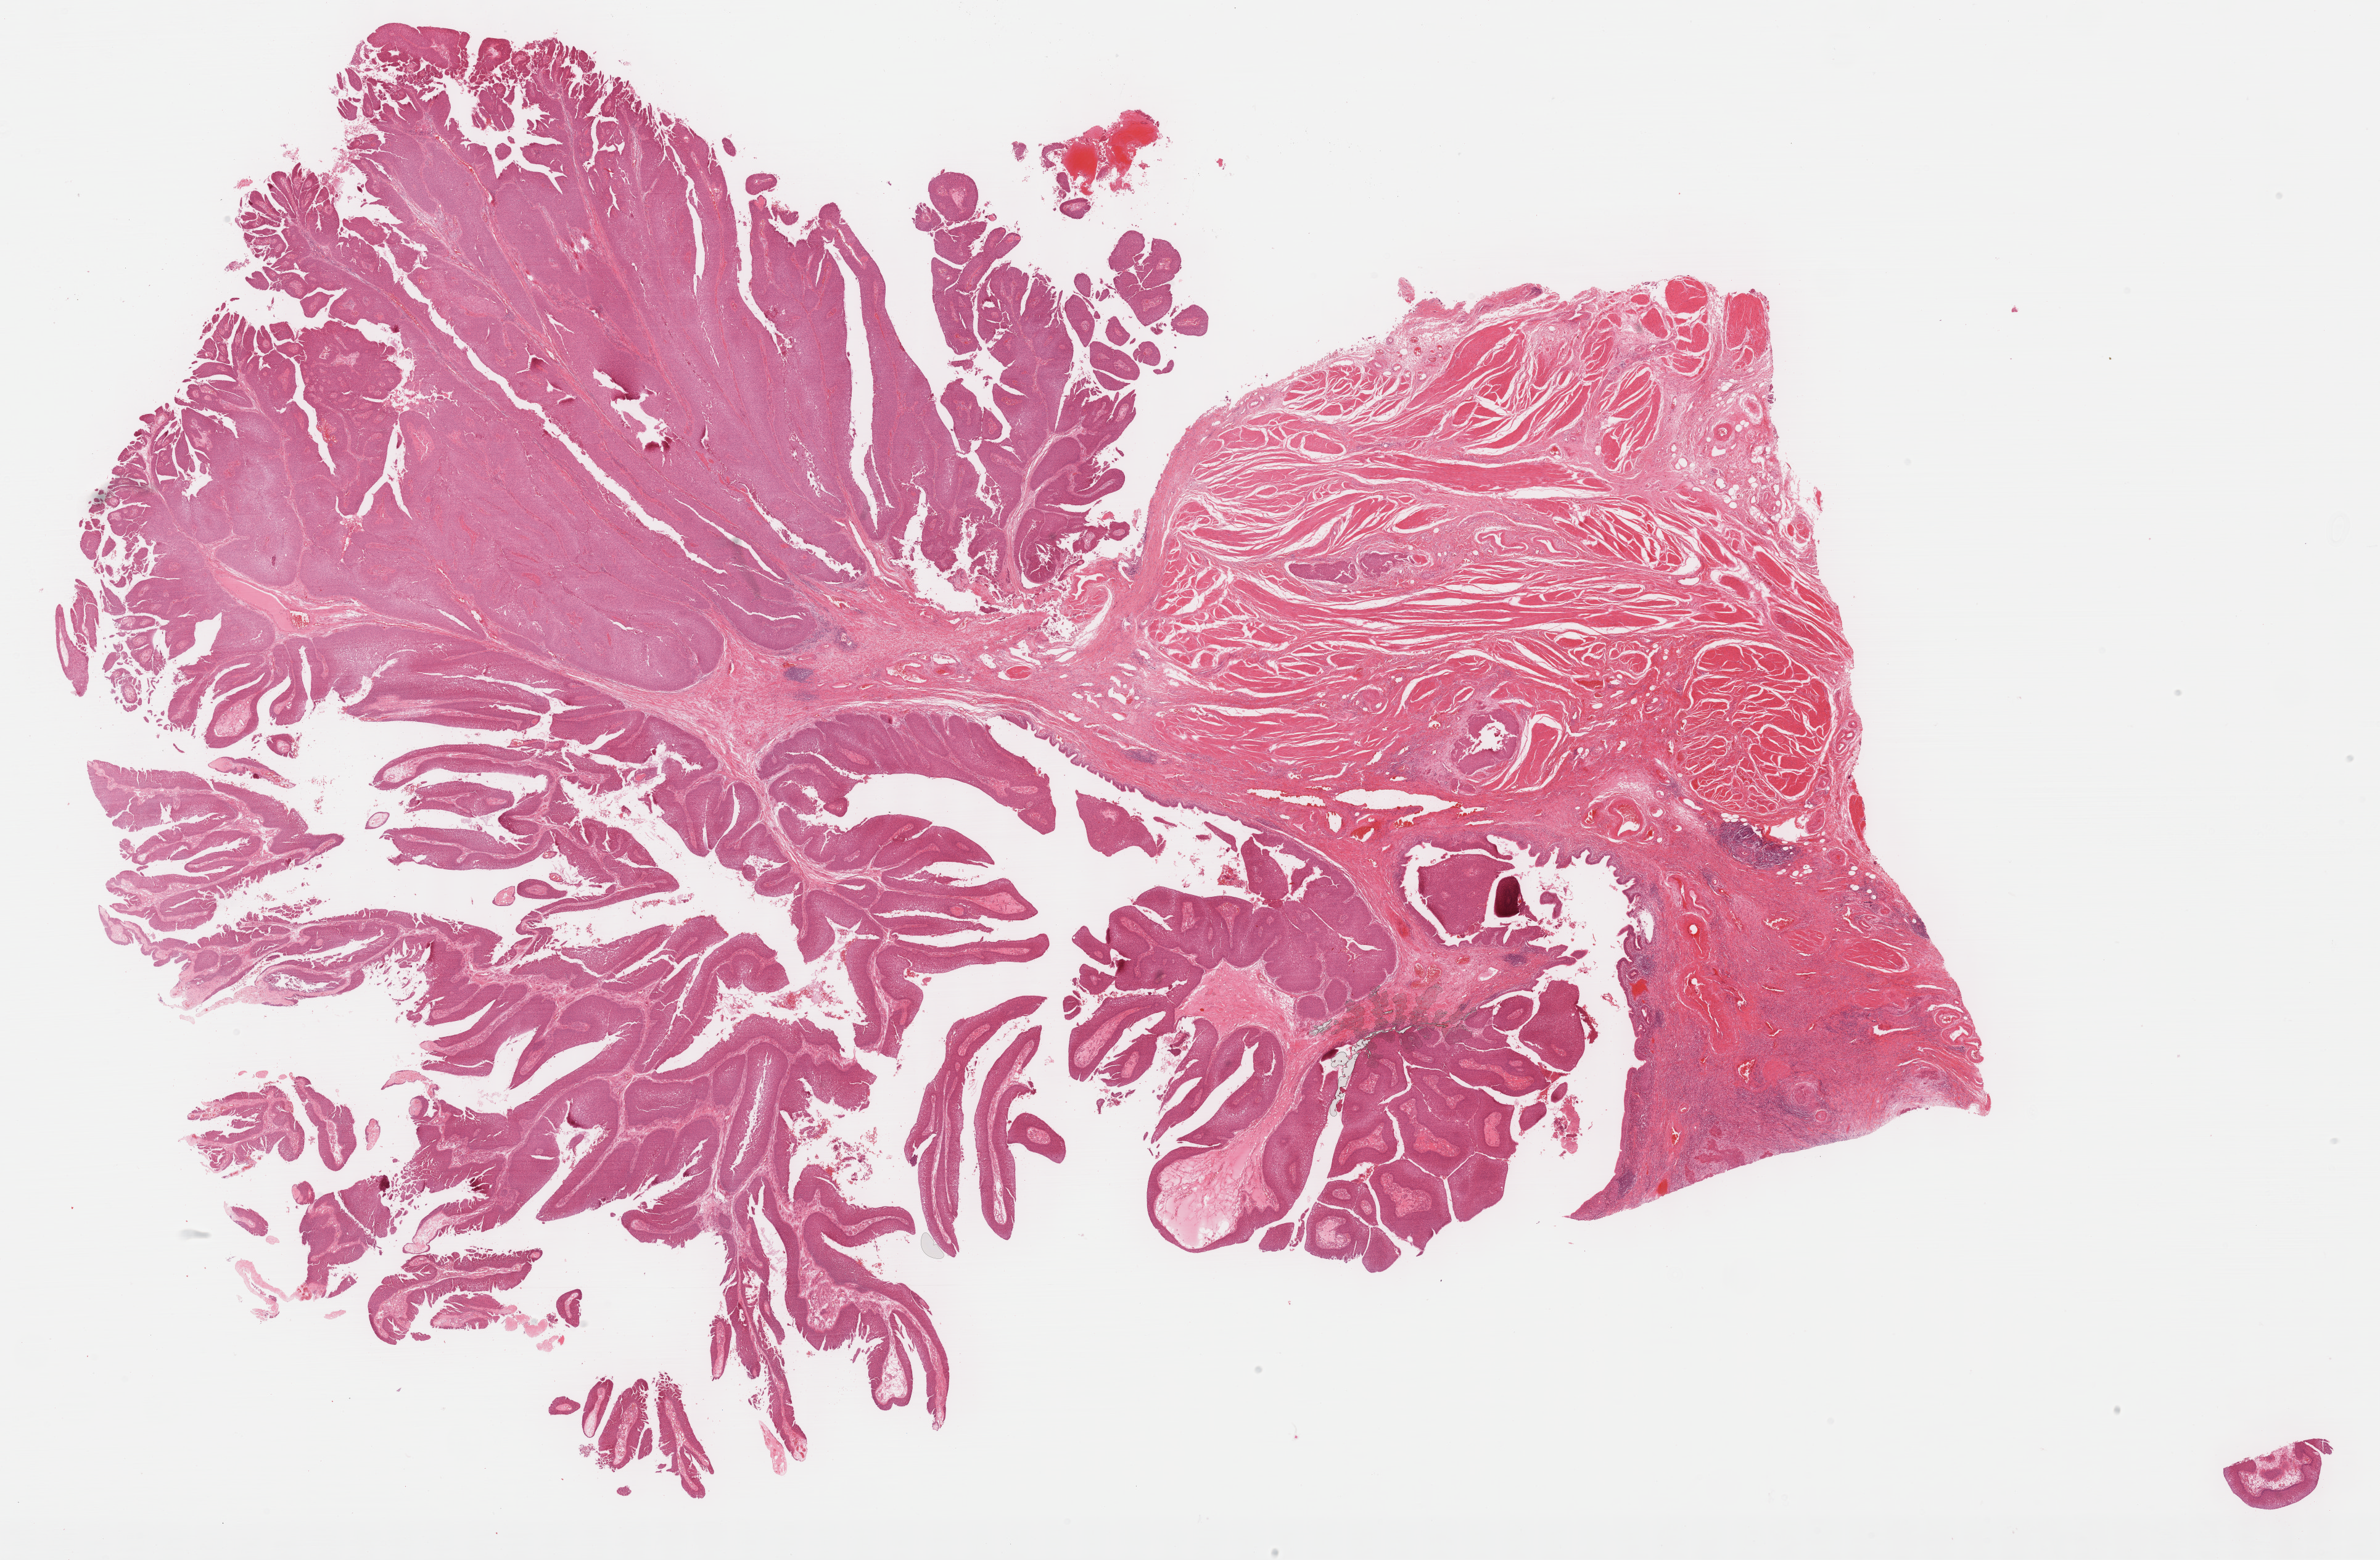
Whole-slide histology image, Hematoxylin and eosin (H&E) stained — low-resolution overview of the scanned area, about 31.2 x 20.5 mm; formalin-fixed paraffin-embedded (FFPE) diagnostic section; primary tumour sample from the bladder. Patient: male, age at initial diagnosis 70 years. Histologic grade: high grade.
Pathologic diagnosis: Transitional cell carcinoma. AJCC pathologic stage: III (6th edition). TNM: T4a NX MX.